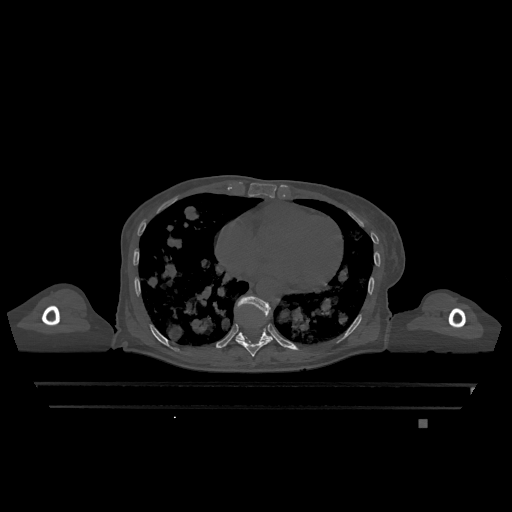
CT including the spine, one axial slice; bone window (W 1800 / L 400 HU); 0.5 mm slice thickness; 512 × 512 image matrix, field of view 500 × 500 mm. Female patient, age 74 years. From the clinical record (not read from this slice): primary cancer: lung.
Annotated regions visible in this slice (semi-automatic segmentation, software-assisted and operator-edited):
- T10 vertebra: bounding box <236,296,273,341> (left, top, right, bottom; pixels)
- T9 vertebra: <236,318,272,357>